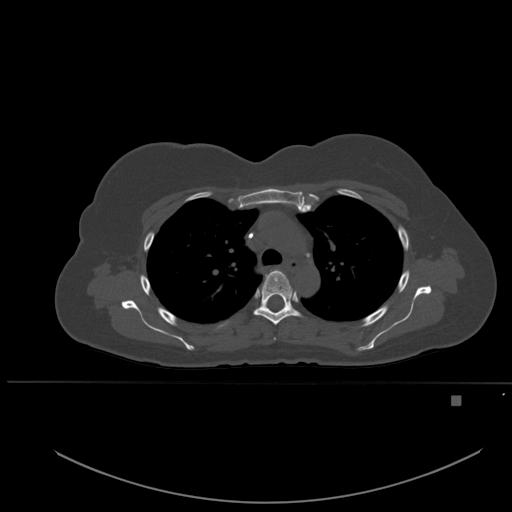
CT including the spine, one axial slice. Position 380 of 651 along the scan axis. Bone window (W 1800 / L 400 HU). 1.5 mm slice thickness. 512 × 512 image matrix, field of view 443 × 443 mm. Female patient, age 49 years. Case-level facts recorded for this patient, not image findings: primary cancer: breast.
Structures marked on this image (semi-automatically segmented with operator editing):
- T3 vertebra: bounding box <274,338,276,340> (left, top, right, bottom; pixels)
- T4 vertebra: <253,270,302,325>